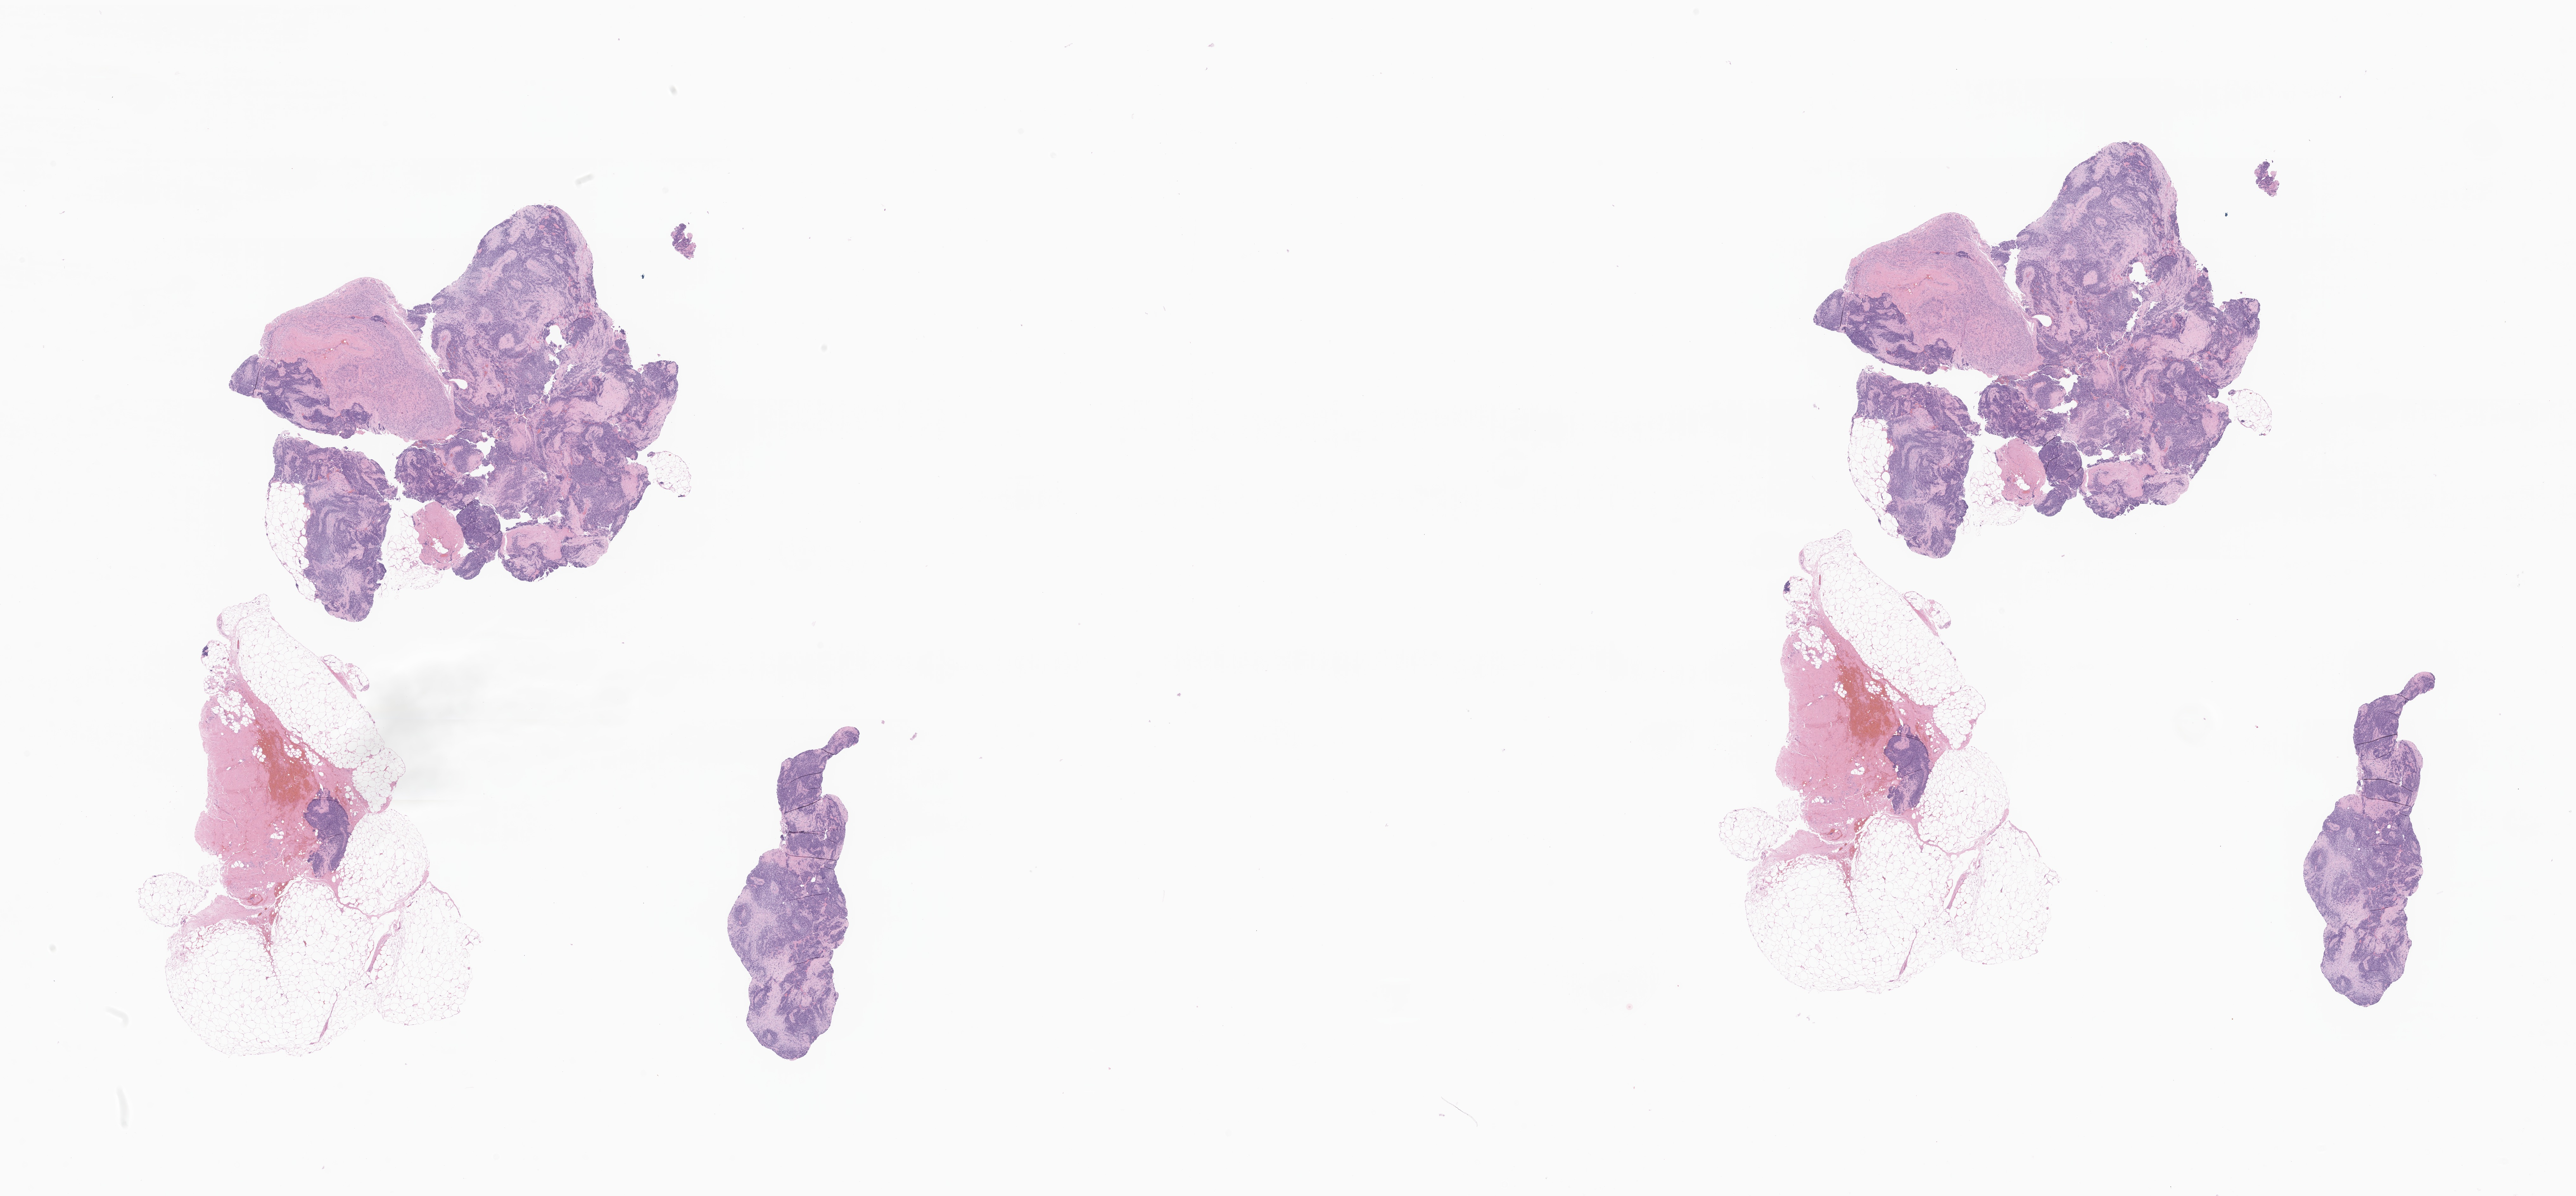
Whole-slide image, hematoxylin and eosin (H&E) stain of tumor tissue from the long bone of lower limb — whole scanned area (about 34.3 x 15.9 mm) shown as a low-resolution overview, formalin-fixed paraffin-embedded section. Female patient, age 91 months (7 years 7 months).
- diagnosis: Alveolar rhabdomyosarcoma